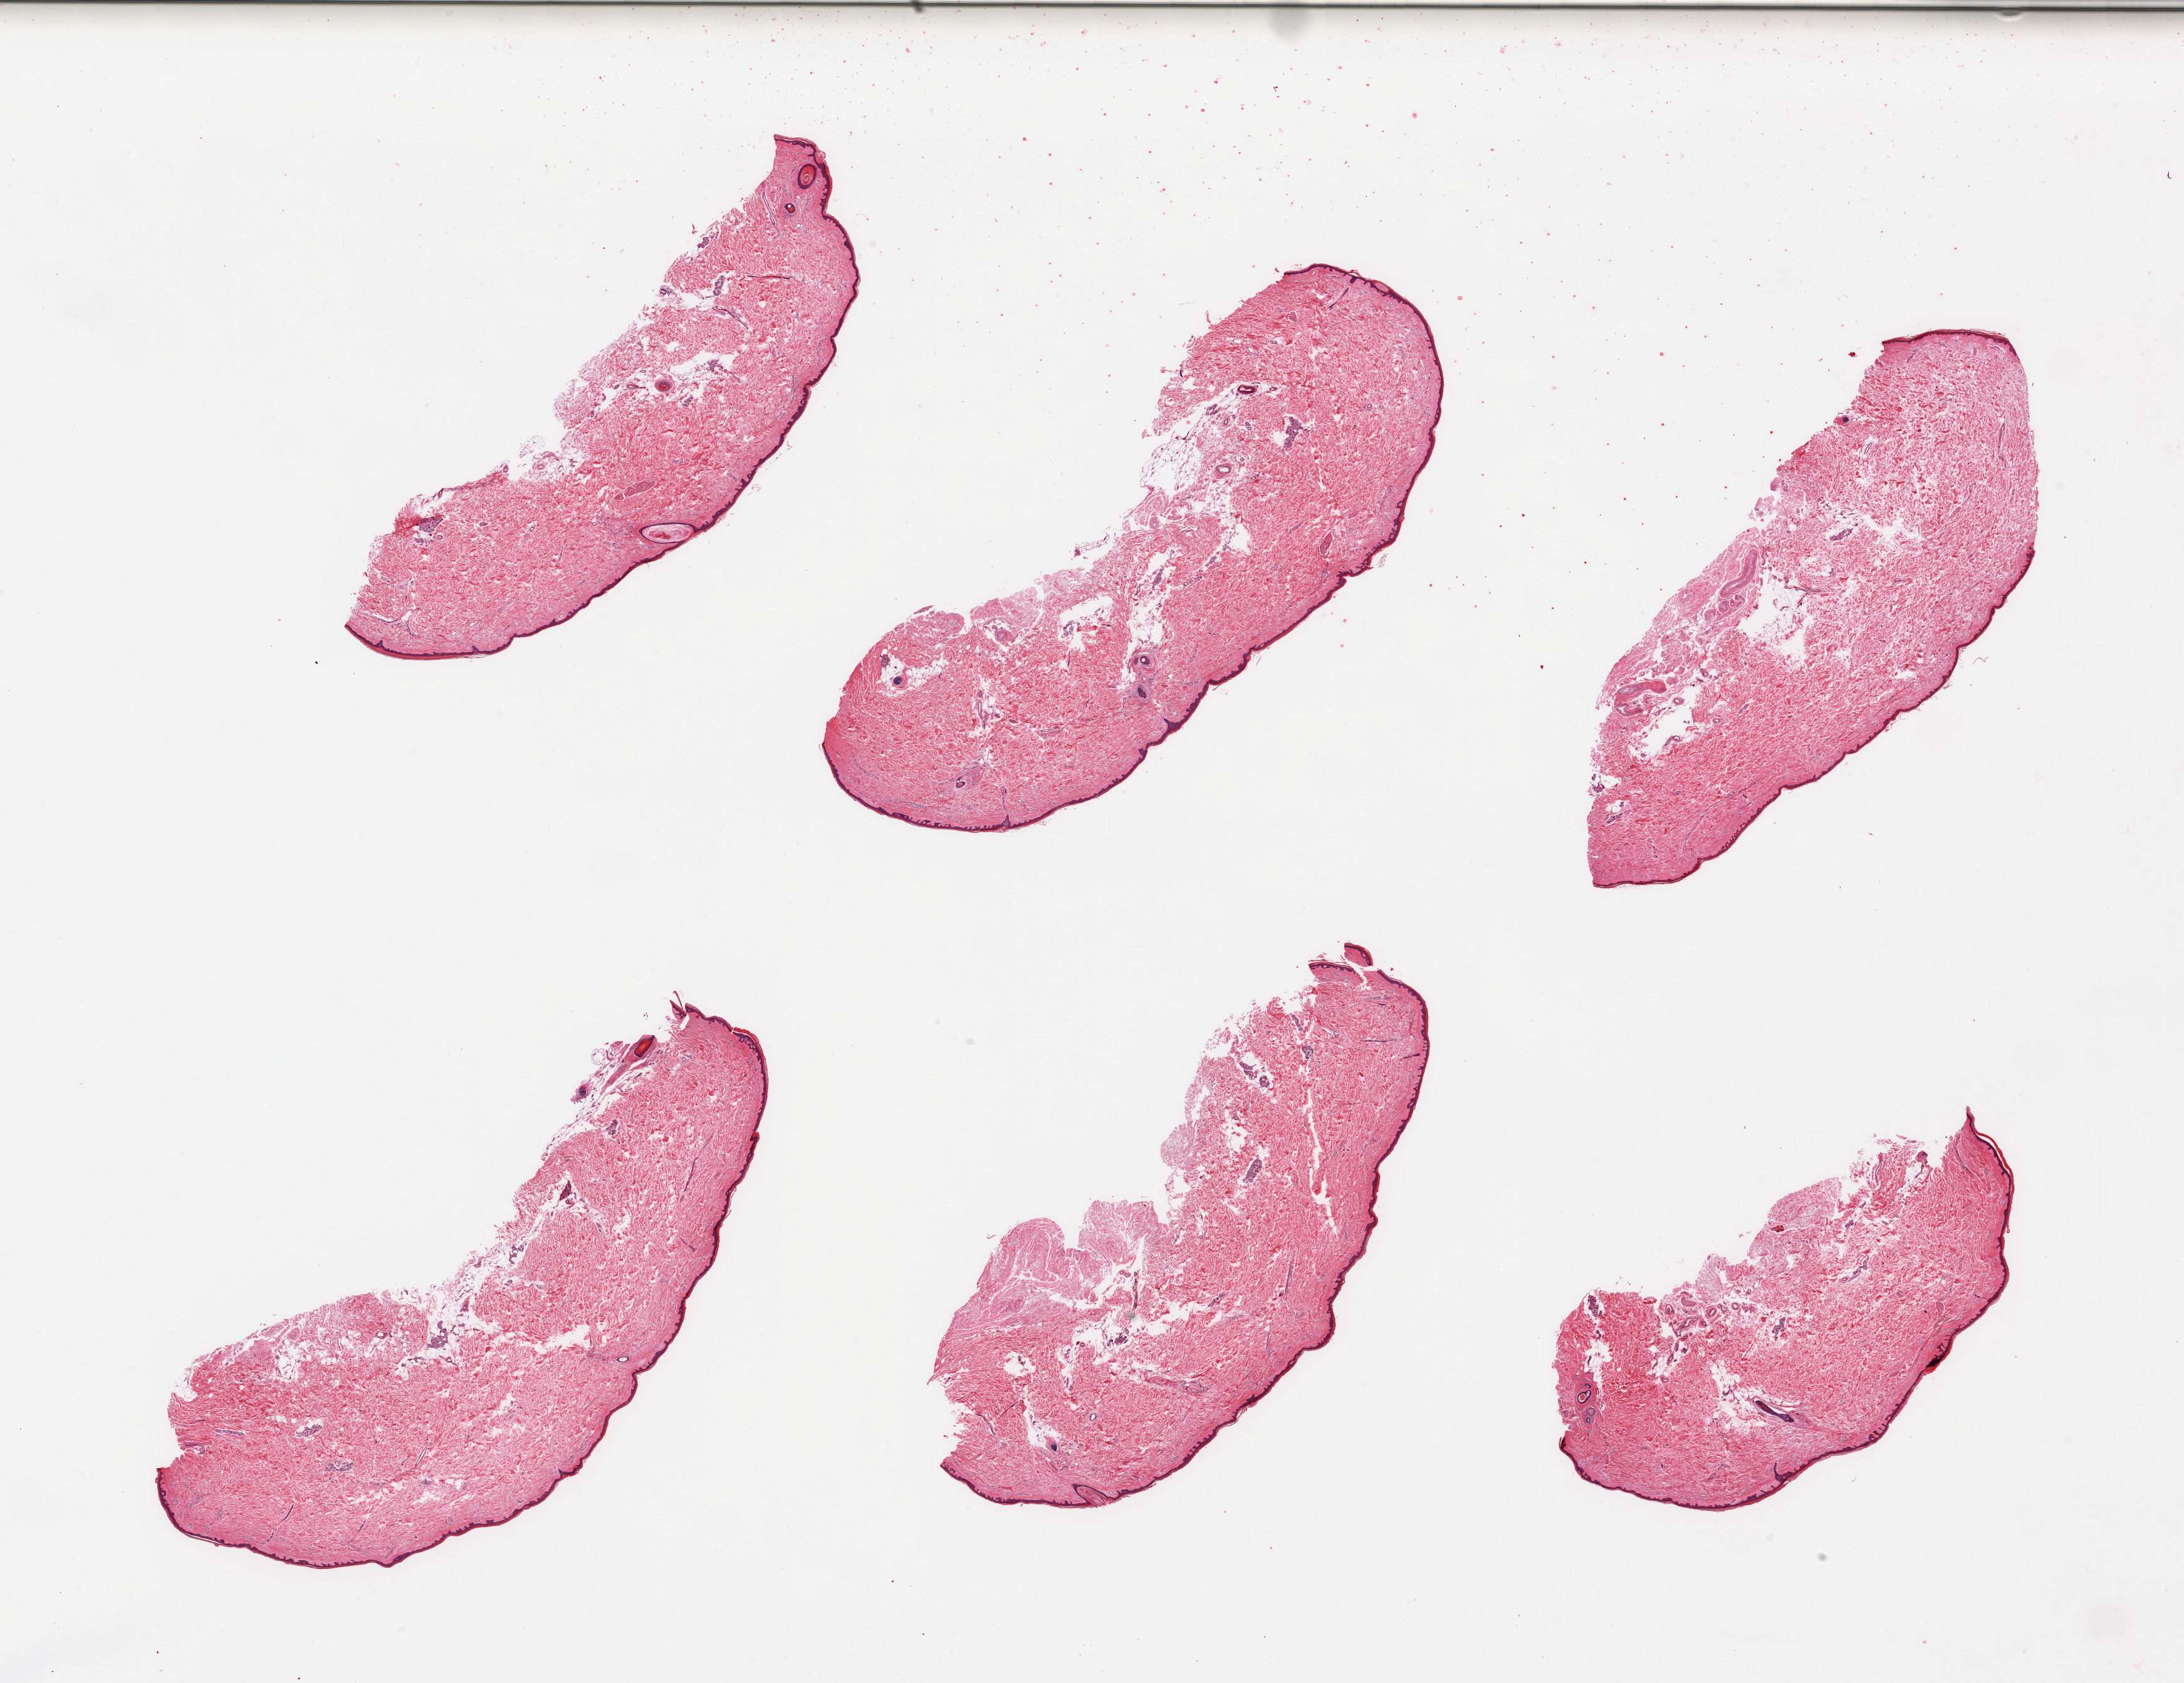
Haematoxylin and eosin whole-slide image — a low-resolution overview of the entire scanned area, about 27.6 x 21.2 mm. PAXgene-fixed, paraffin-embedded tissue. Target tissue: skin of lower leg. Donor tissue sample. Donor sex: female.
Reviewer comment on this tissue sample: 6 pieces, minimal dermal fat; squamous epithelium up to ~35 microns.